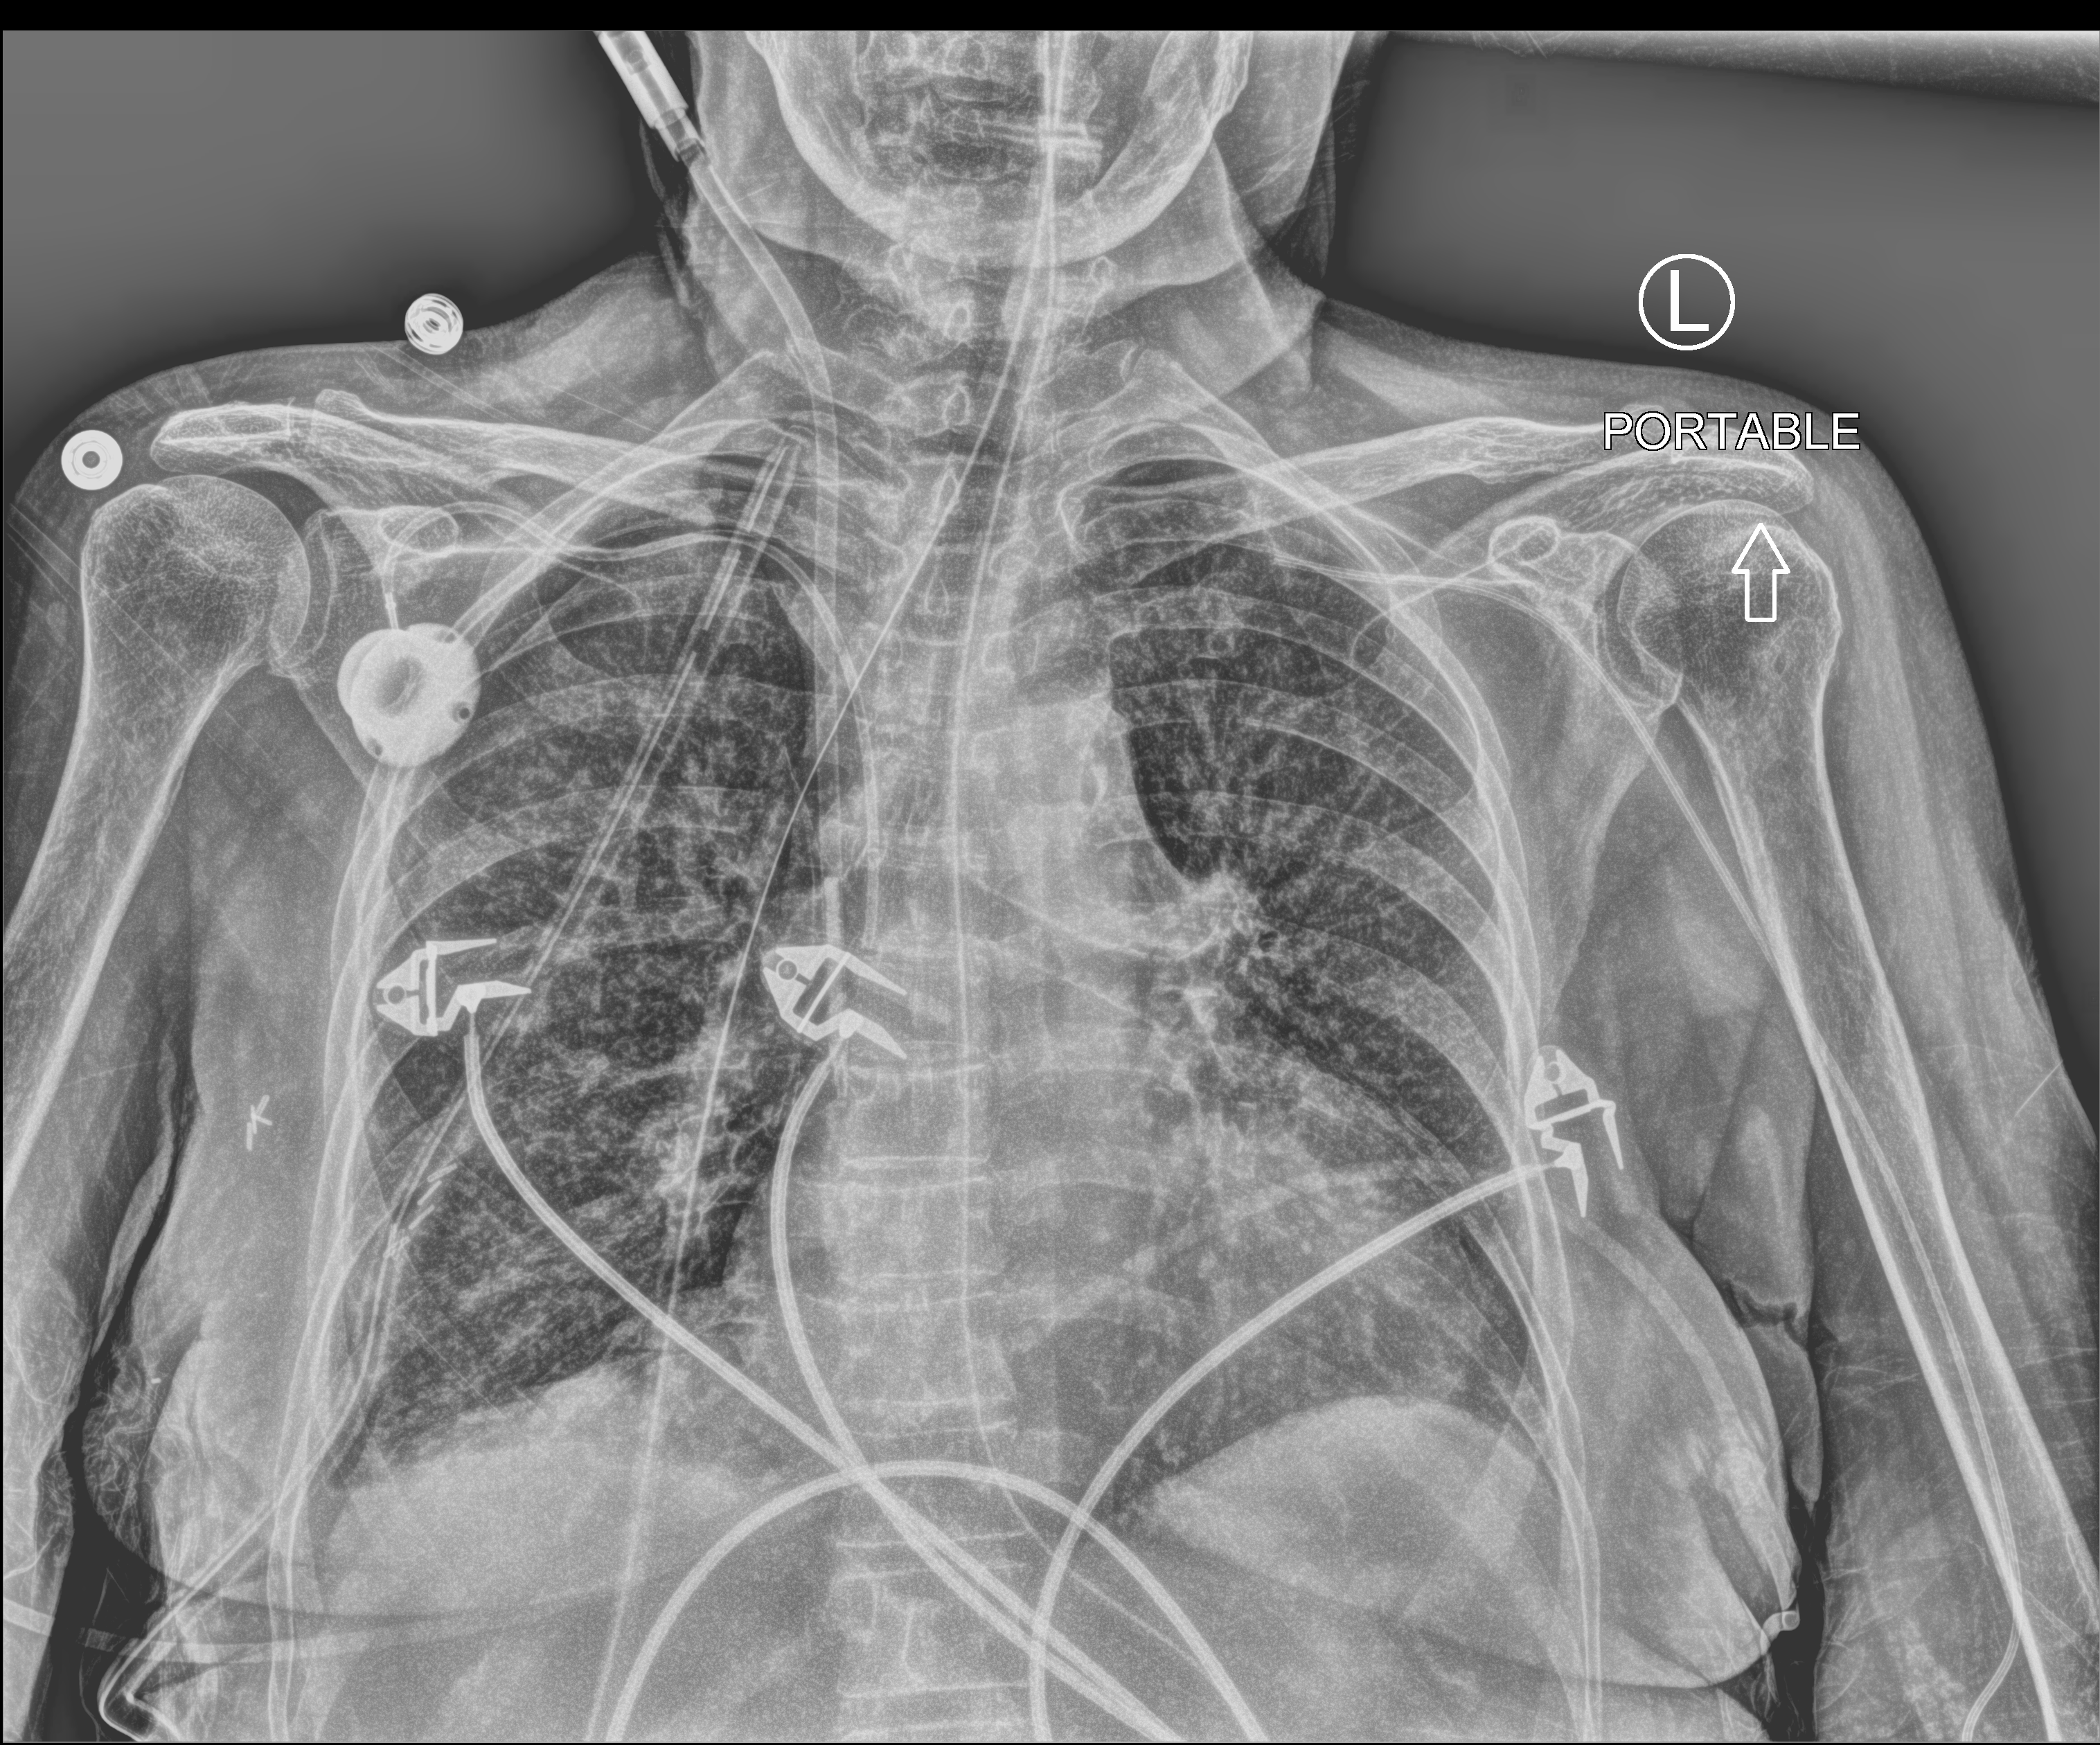
Chest X-ray (portable), anteroposterior (AP) projection. Patient hospitalised with COVID-19; female, aged 60–74 years.
Hospital-stay facts (about this admission, not read from this image; timing relative to this image not recorded):
- mechanically ventilated during this hospital stay: yes
- admitted to intensive care during this hospital stay: yes